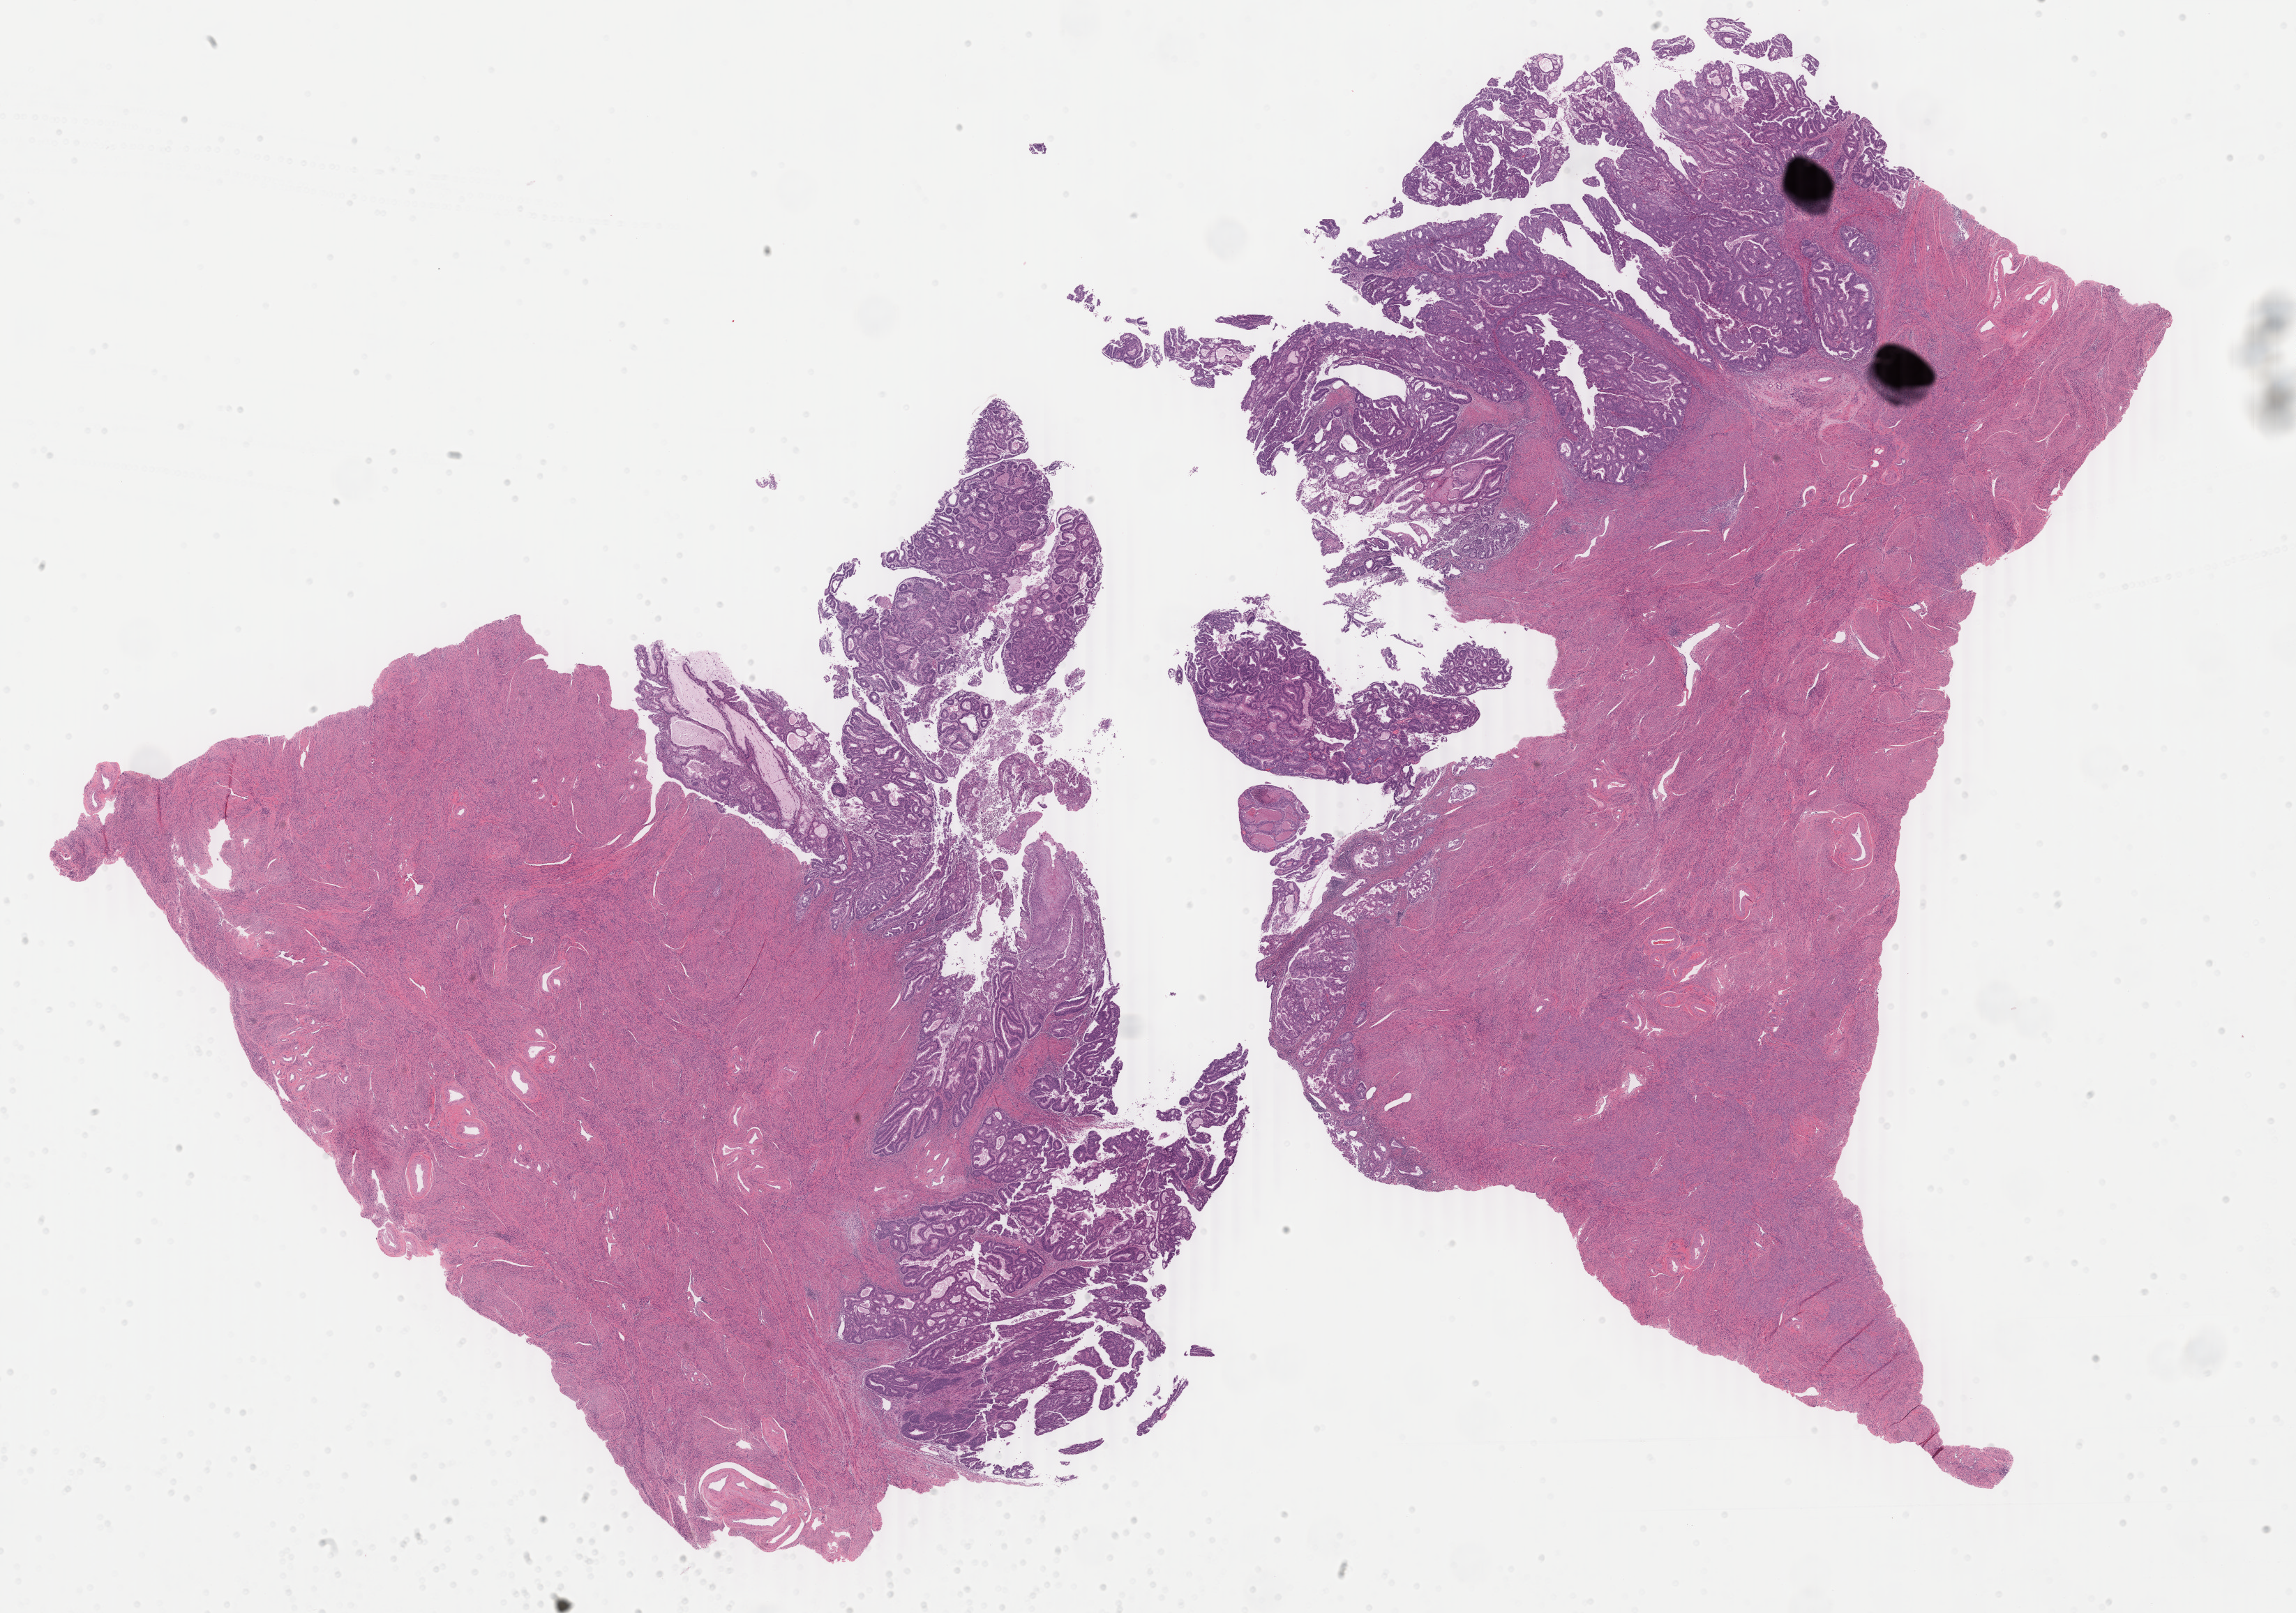
H&E-stained whole-slide image, whole scanned area (about 26.2 x 18.4 mm) shown as a low-resolution overview. Formalin-fixed paraffin-embedded (FFPE) diagnostic section. Sample: primary tumour, uterus. Female, age 60 years at initial diagnosis. Histologic grade: G2 (moderately differentiated).
• pathologic diagnosis: Endometrioid adenocarcinoma, NOS (endometrium)
• FIGO stage: IB